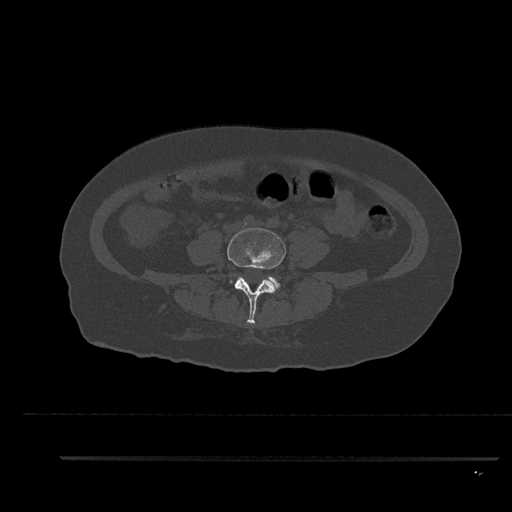
CT including the spine, one axial slice. Position 5 of 797 along the scan axis. Bone window (W 1800 / L 400 HU). 0.5 mm slice thickness. 512 × 512 image matrix, field of view 408 × 408 mm. Patient: female, 44 years. Case-level facts recorded for this patient, not image findings: primary cancer: renal; vertebrae with lytic lesions (as recorded): L1.
Annotated regions visible in this slice (semi-automatic segmentation, software-assisted and operator-edited):
- L4 vertebra: bounding box (x1, y1, x2, y2) in pixels: (227, 228, 286, 324)